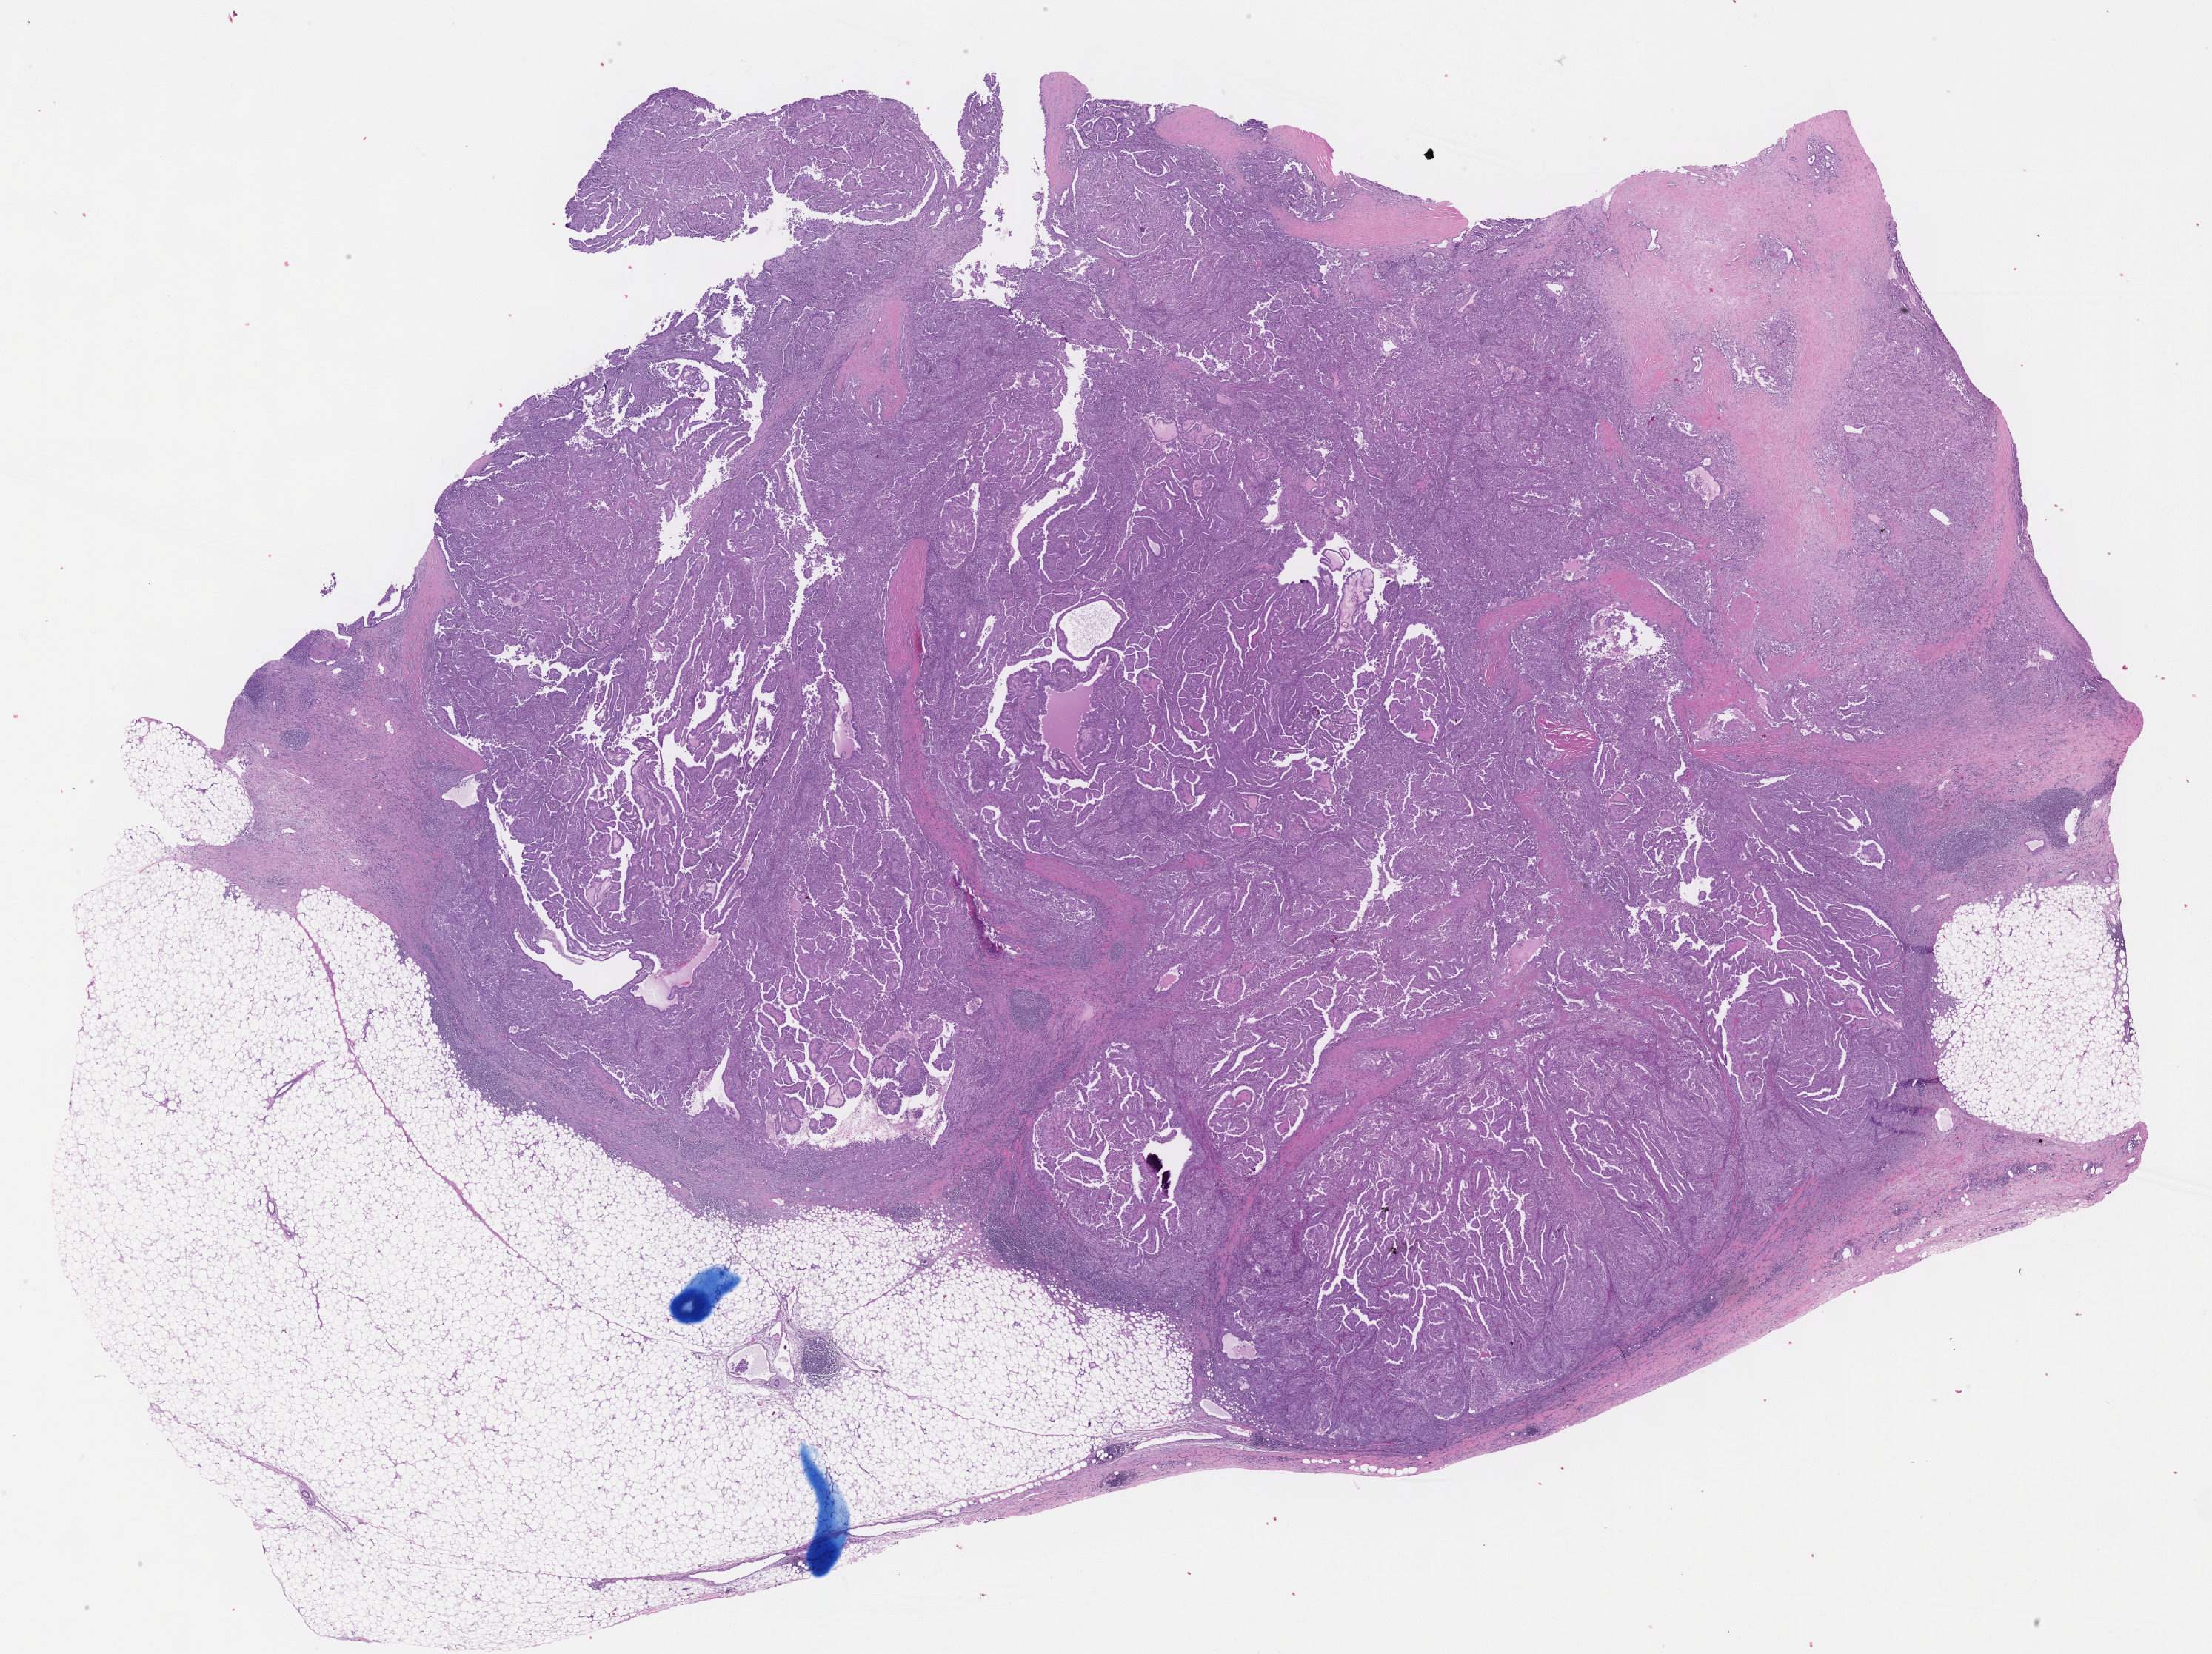
Digitized H&E tissue section (whole slide) — whole scanned area (about 24.2 x 18.1 mm, acquisition: 40x scan) shown as a low-resolution overview. Formalin-fixed paraffin-embedded (FFPE) diagnostic section. Primary tumour sample from the kidney. Patient: female, age at initial diagnosis 54 years.
* lymph nodes positive (case pathology): 1 of 5 examined
* laterality: left
* histologic diagnosis: Papillary adenocarcinoma, NOS
* AJCC pathologic stage: III